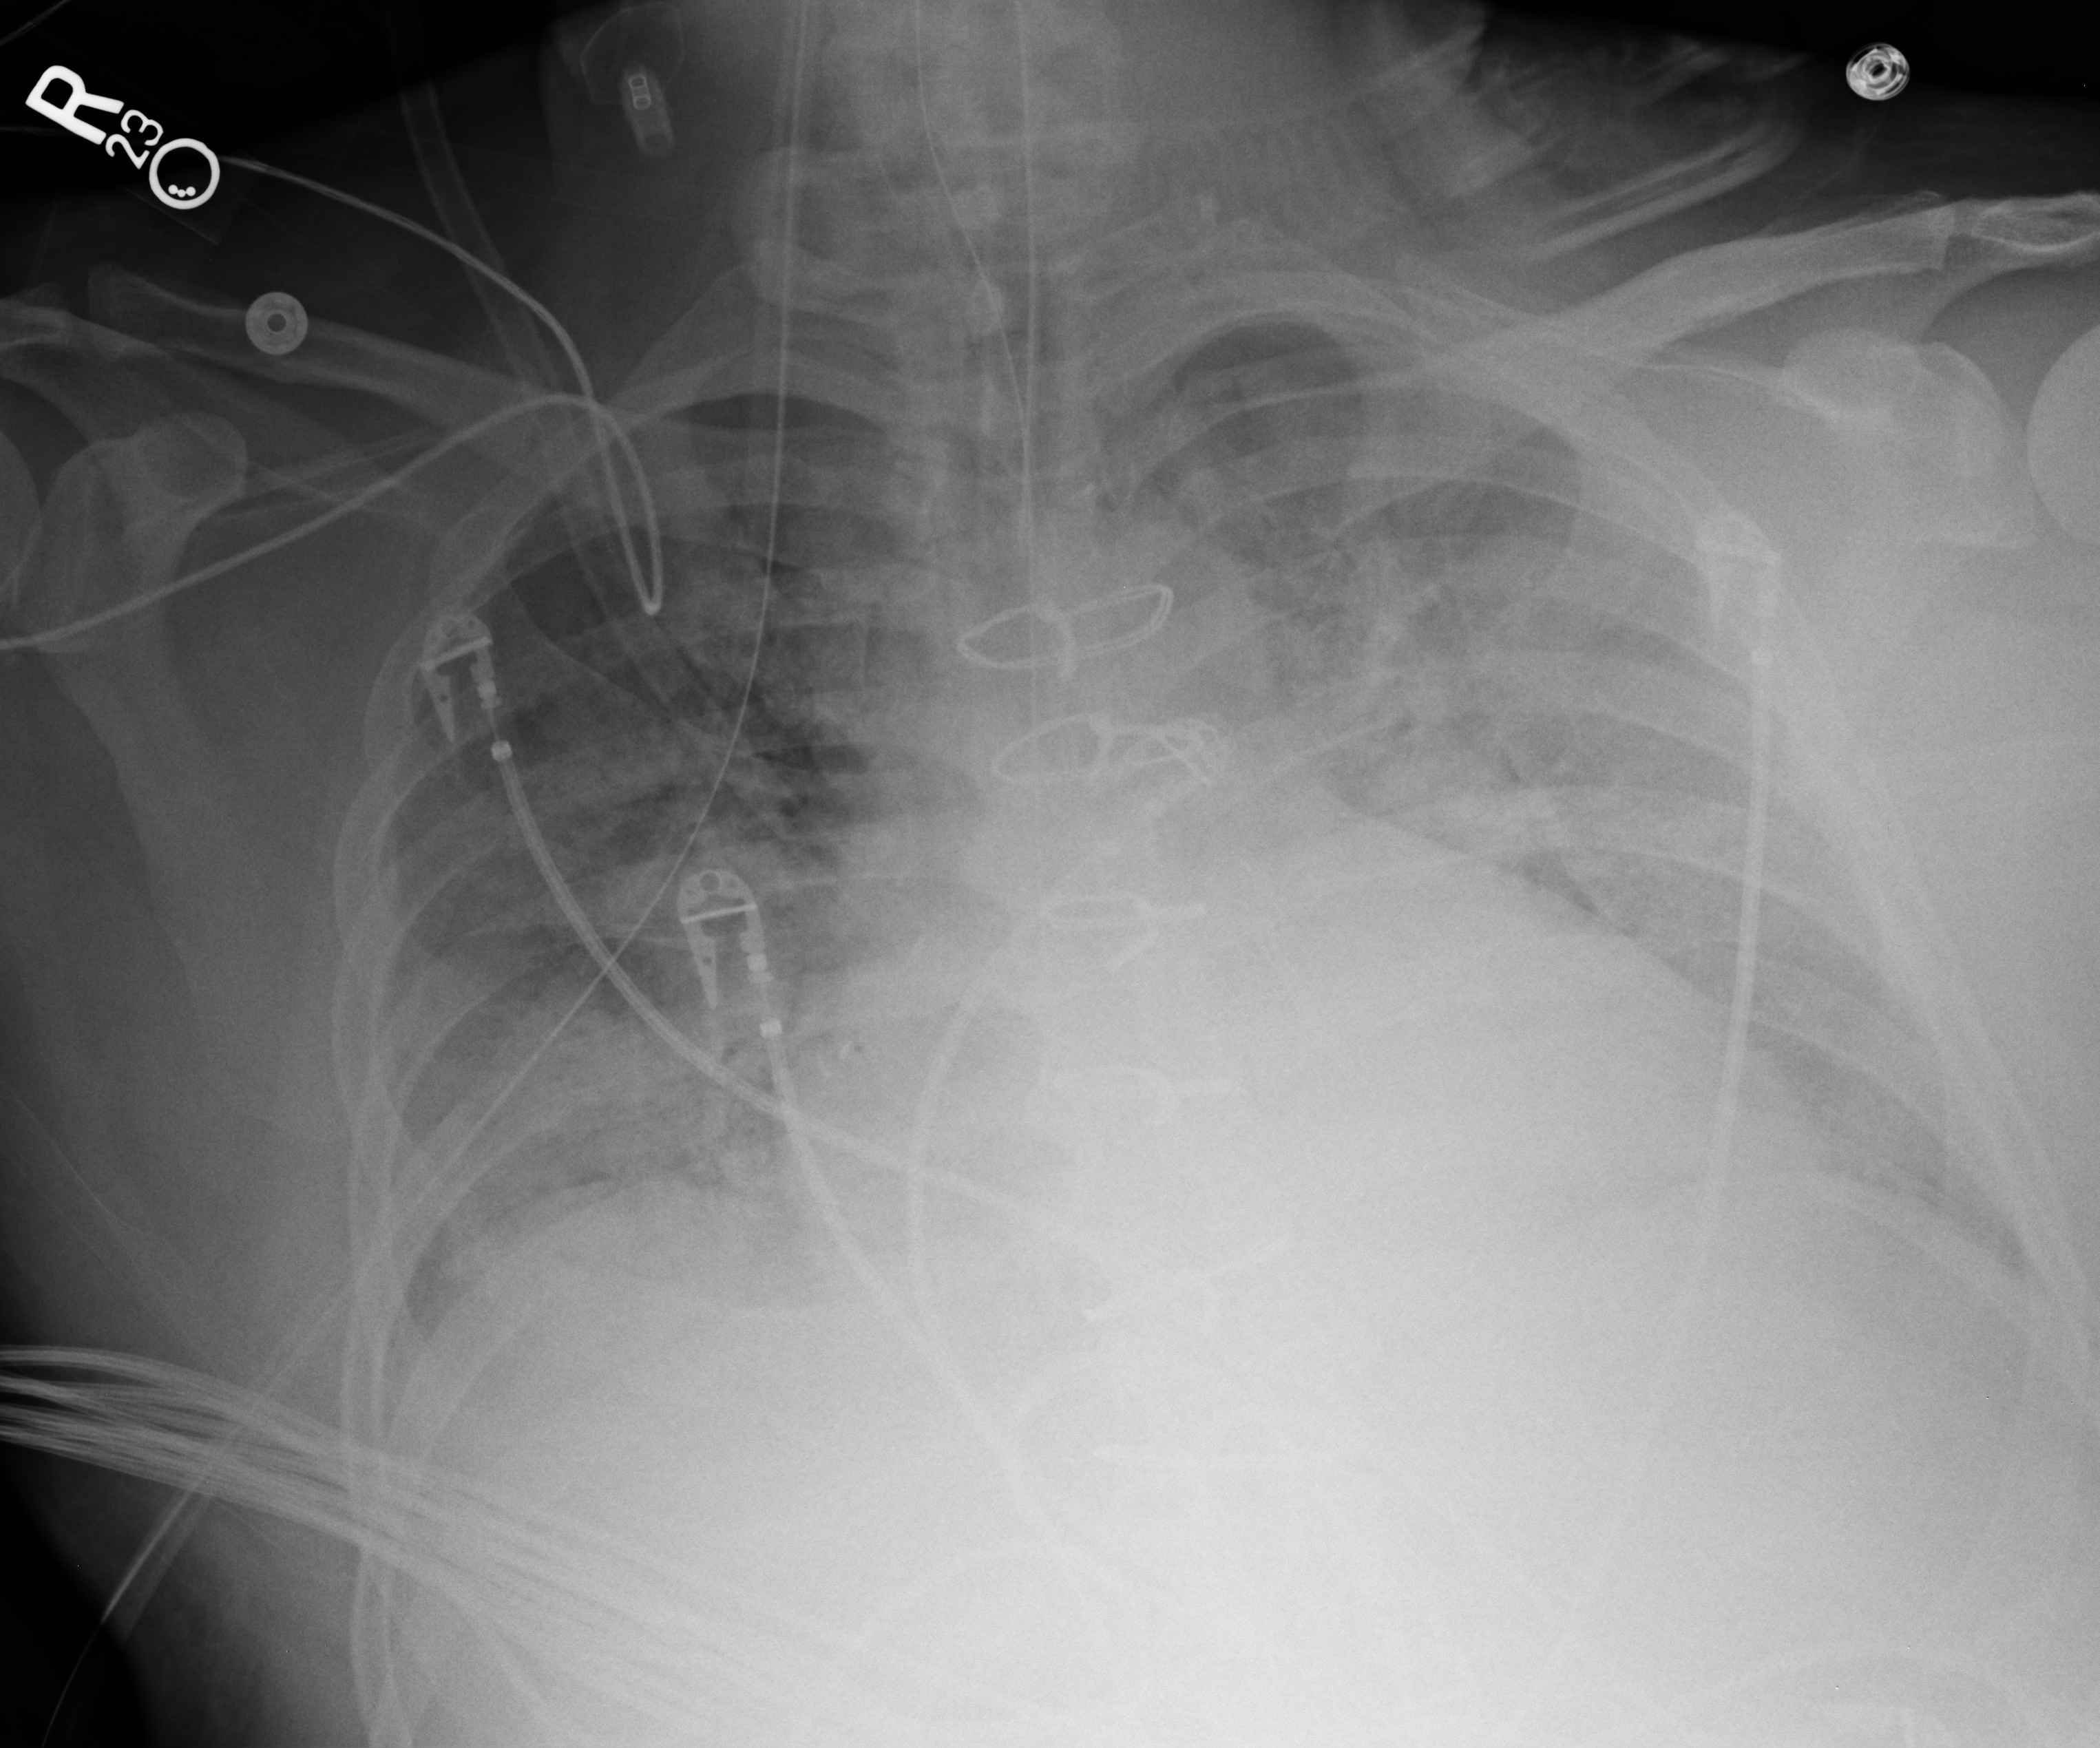
Portable chest radiograph; anteroposterior (AP) projection. Patient hospitalised with COVID-19, aged 18–59 years.
From the hospital-stay record, not from the radiograph (when in the stay this image was taken is not recorded):
- mechanically ventilated during this hospital stay: yes
- smoking status (admission record): never
- admitted to intensive care during this hospital stay: yes